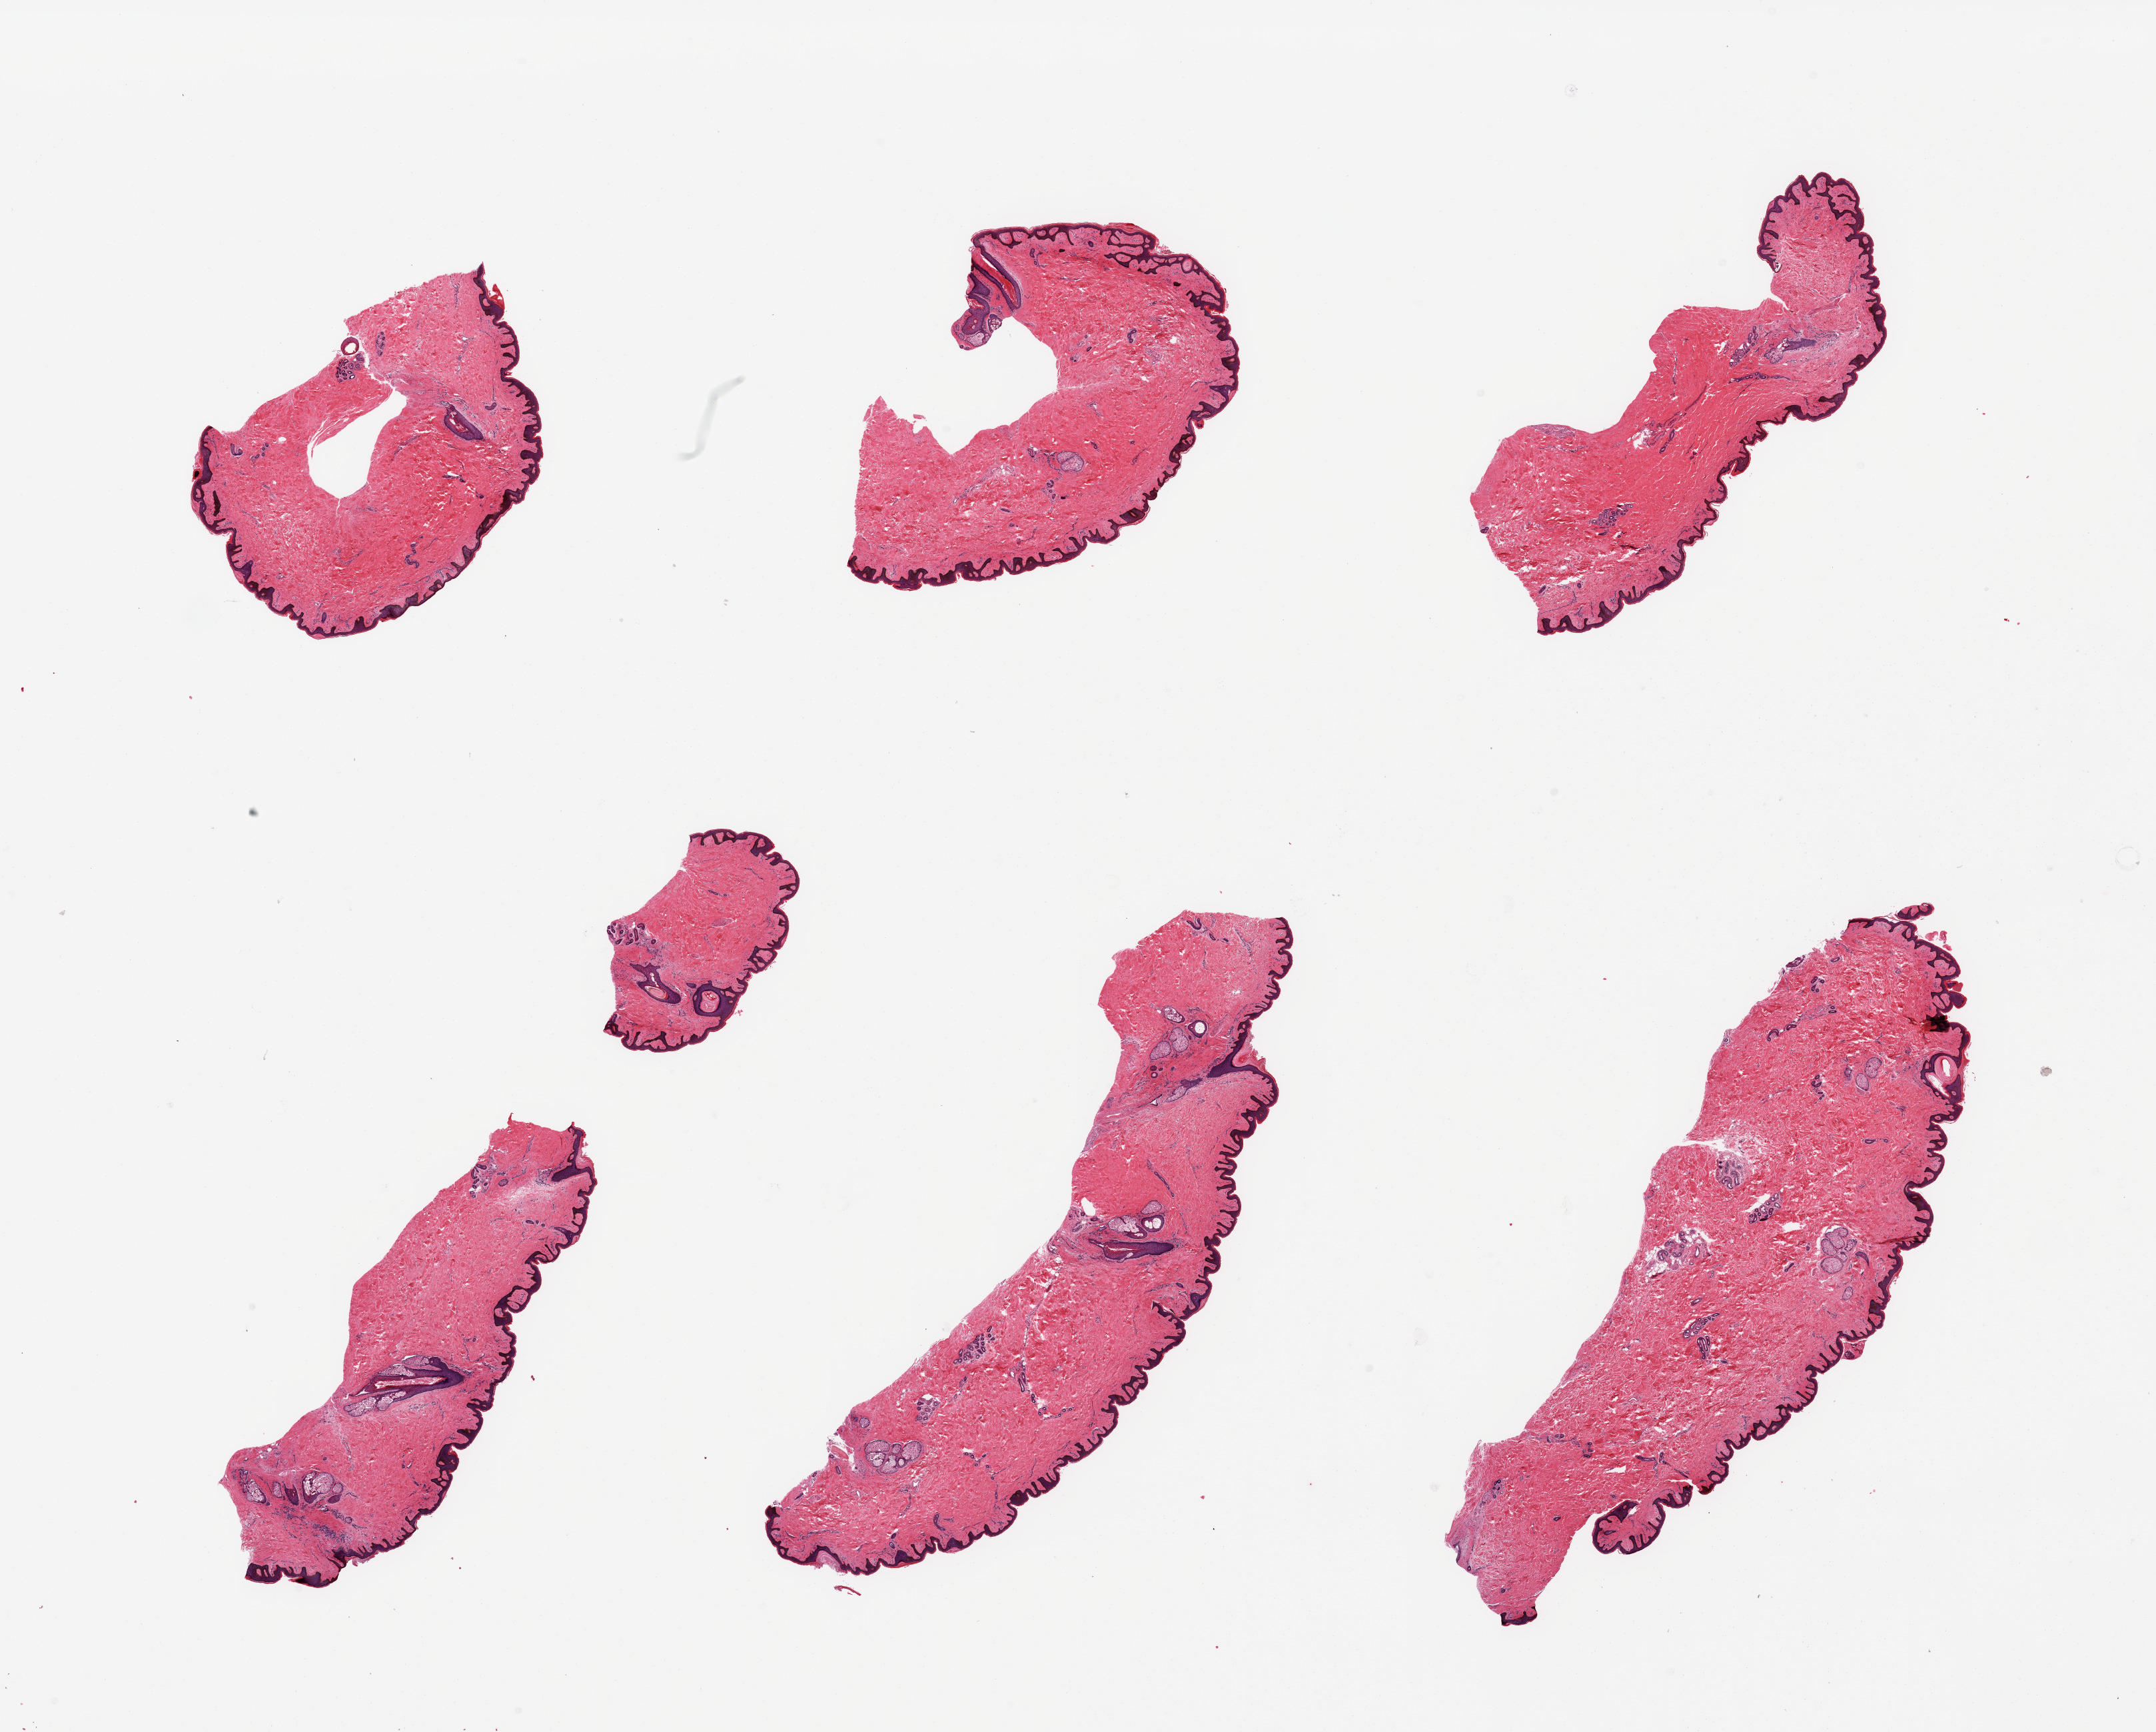
Whole-slide image, hematoxylin and eosin (H&E) stain, low-resolution overview of the scanned area, about 25.6 x 20.6 mm (slide scanned at 20x), PAXgene-fixed paraffin-embedded (PFPE) section, target tissue: skin of suprapubic region, donor tissue sample.
- reviewer comment on this tissue sample: 6 pieces, no significant dermal fat; squamous epithelium is ~35-40 microns